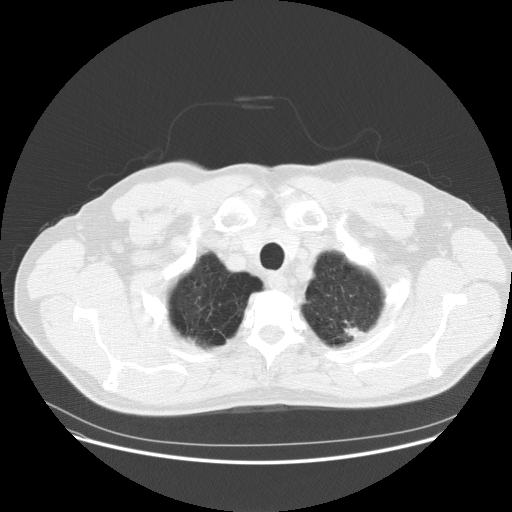
Chest CT (low-dose screening protocol), one axial image, baseline annual screen, lung window (W 1500 / L -600 HU), 2.5 mm slice thickness. Male, age 61 years at enrolment. Current smoker at enrolment.
Lesion marked by an expert reader, bounding box (x1, y1, x2, y2) in pixels: (319, 307, 383, 357). The exam's reader record, not a measurement of the box and not confirmed to be the same lesion: non-calcified nodule or mass ≥4 mm, left upper lobe, 12 × 6 mm, poorly defined margins, soft tissue attenuation. Later outcome: lung cancer diagnosed 317 days after this screen — adenocarcinoma, NOS, left upper lobe, poorly differentiated (G3), stage IIIA (AJCC 6th edition), 30 mm at pathology.